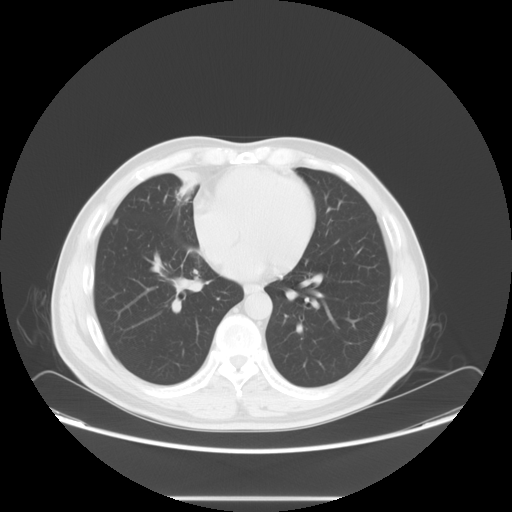
Chest CT, one axial slice. 120 kVp. Lung window (W 1500 / L -600 HU). 5 mm slice thickness. 512 × 512 image matrix. Patient: male, 47 years. Case-level facts recorded for this patient, not image findings: clinical TNM (as recorded): T1c N3 M0.
Structures marked on this image (rectangle marked by the reading radiologist):
- lung tumour (recorded histology: adenocarcinoma): bounding box <162,166,196,206> (left, top, right, bottom; pixels)